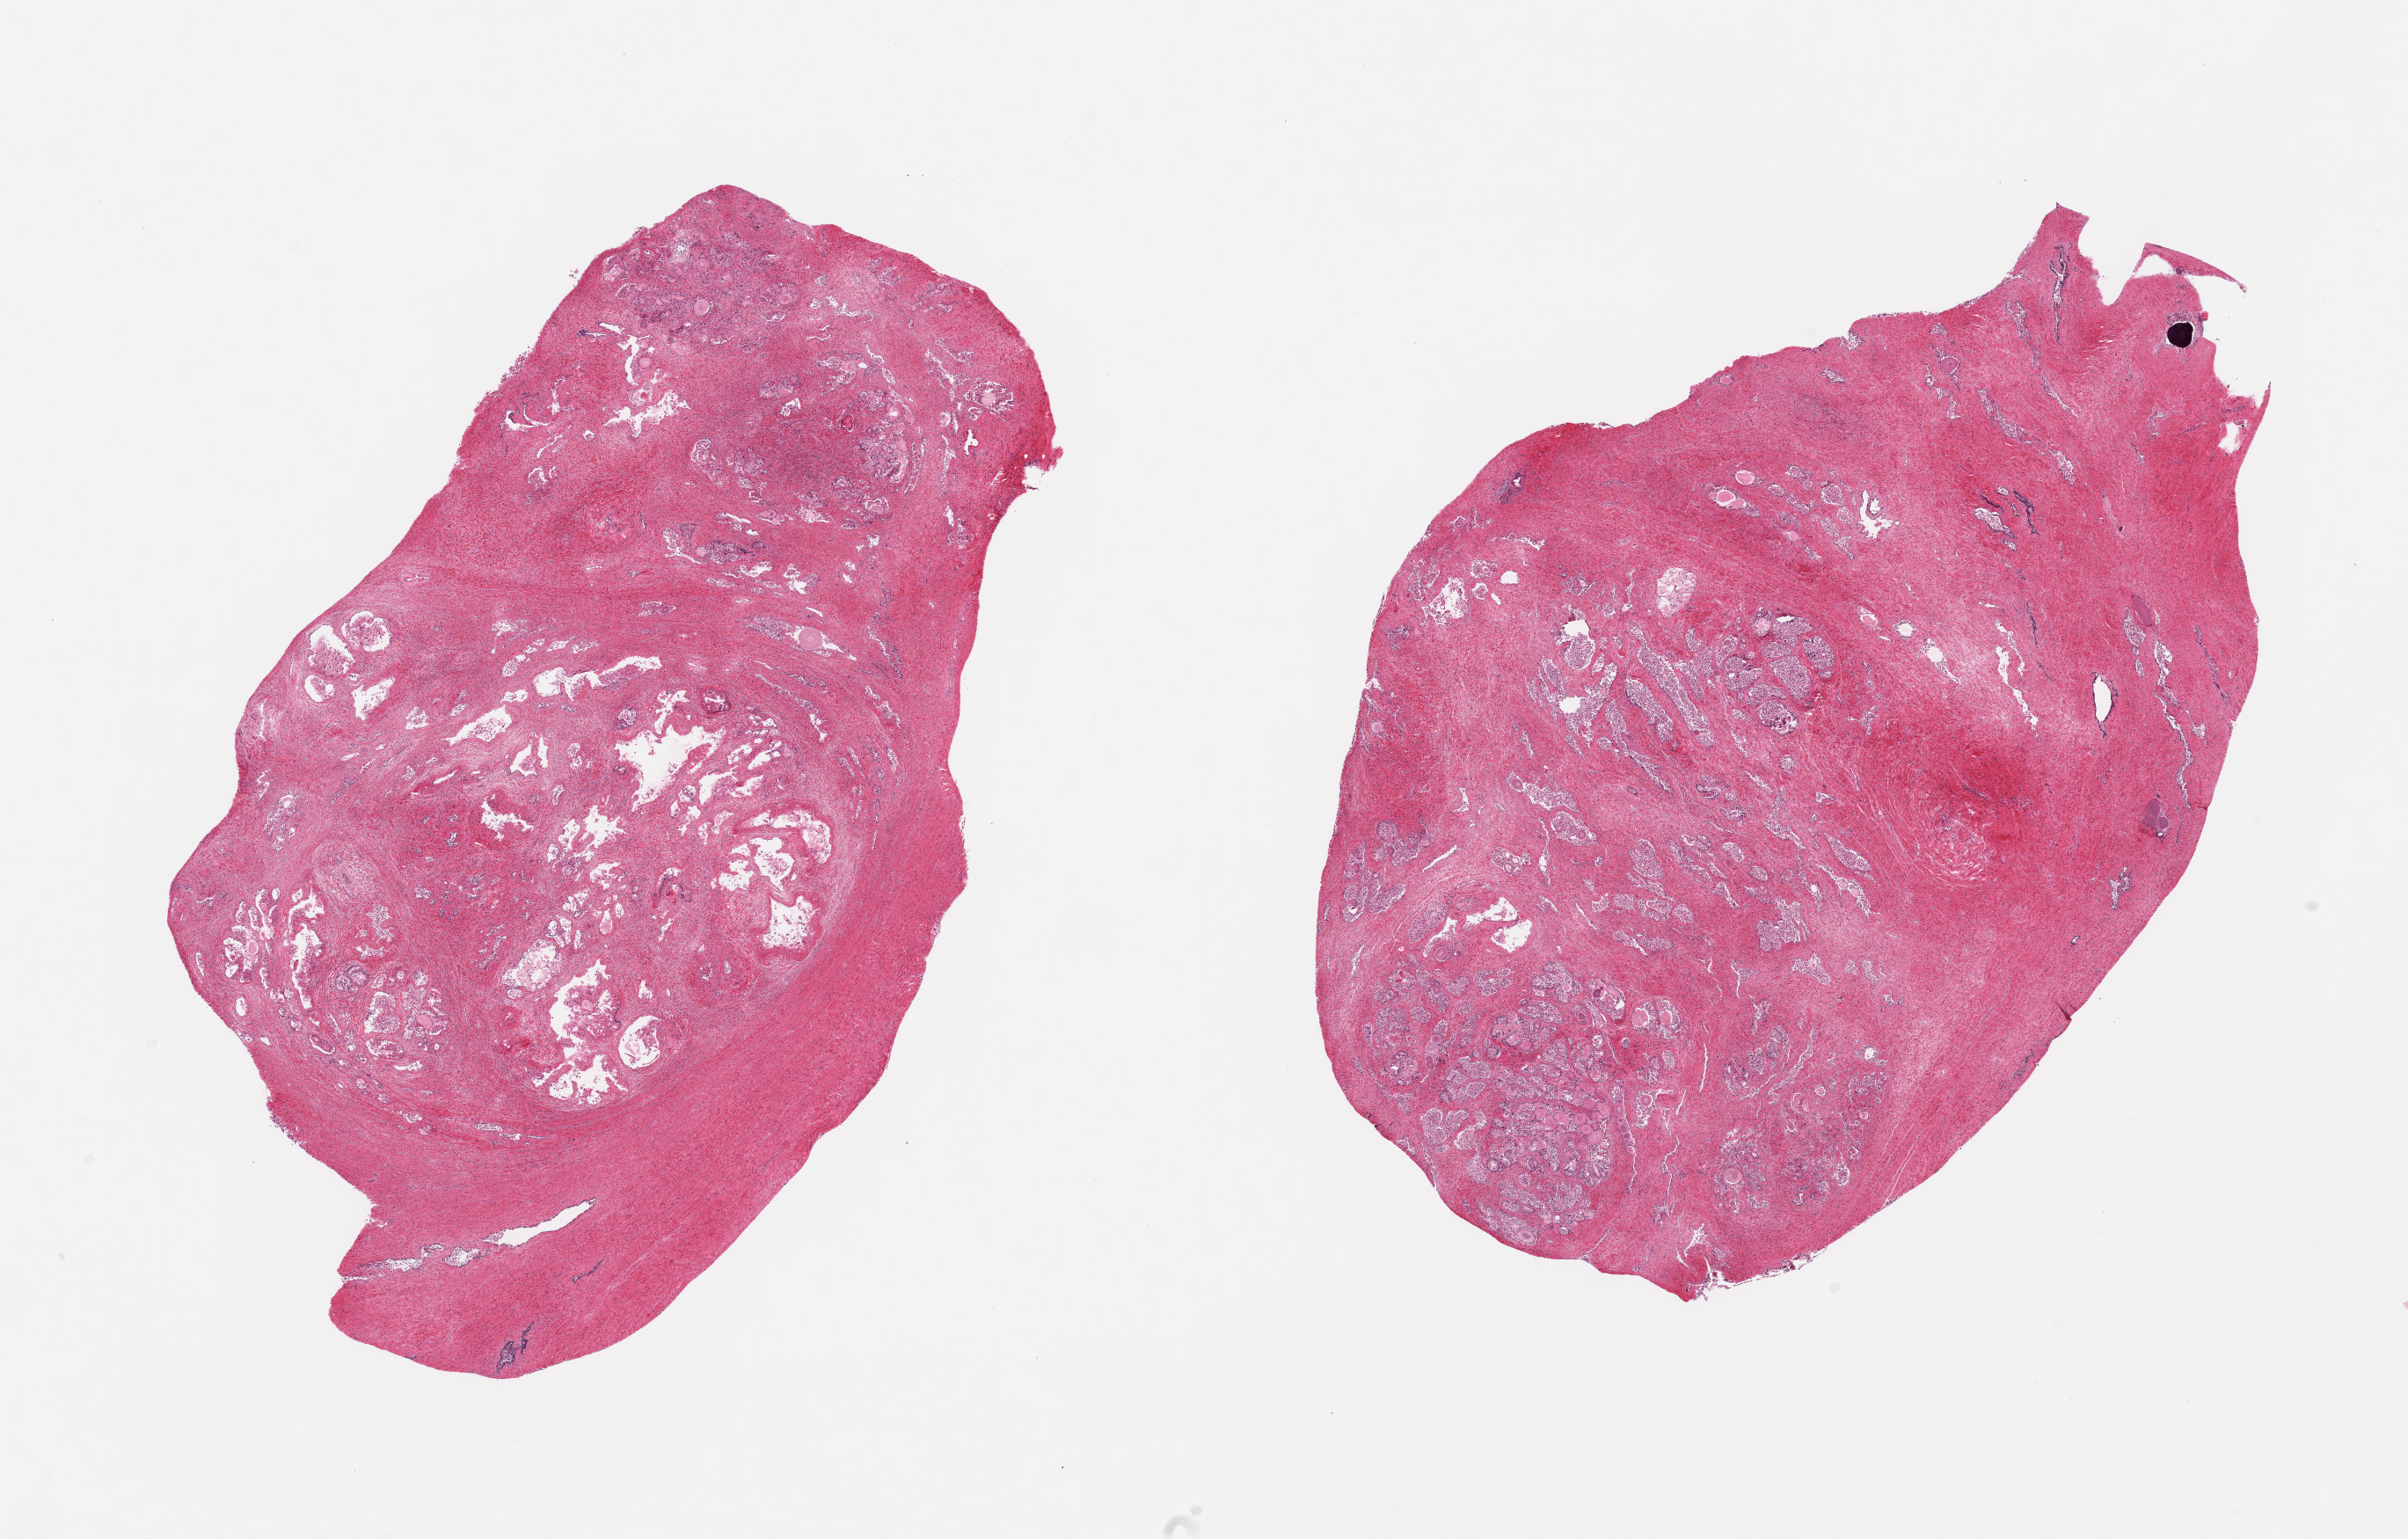
Whole-slide image, hematoxylin and eosin (H&E) stain, brightfield — whole scanned area (about 21.7 x 13.8 mm, acquisition: 20x scan) shown as a low-resolution overview, PAXgene-fixed, paraffin-embedded tissue, section of prostate (target tissue), tissue donor sample. Donor sex: male.
Reviewer comment on this tissue sample: 2 pieces; glandular hypertrophy, but glands autolyzed, stroma intact.